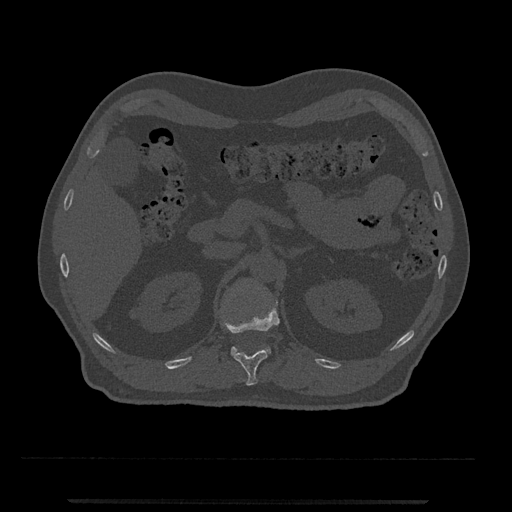
CT including the spine, one axial slice; slice 377 of 797 in the series (ordered by position); reconstruction kernel Br40s/3; 120 kVp; bone window (W 1800 / L 400 HU); 512 × 512 image matrix, field of view 419 × 419 mm. Patient: male, 63 years. Case-level facts recorded for this patient, not image findings: primary cancer: prostate.
Outlined on this slice (semi-automatically segmented with operator editing):
- L1 vertebra: bounding box <231,347,271,356> (left, top, right, bottom; pixels)
- T12 vertebra: <222,300,280,386>